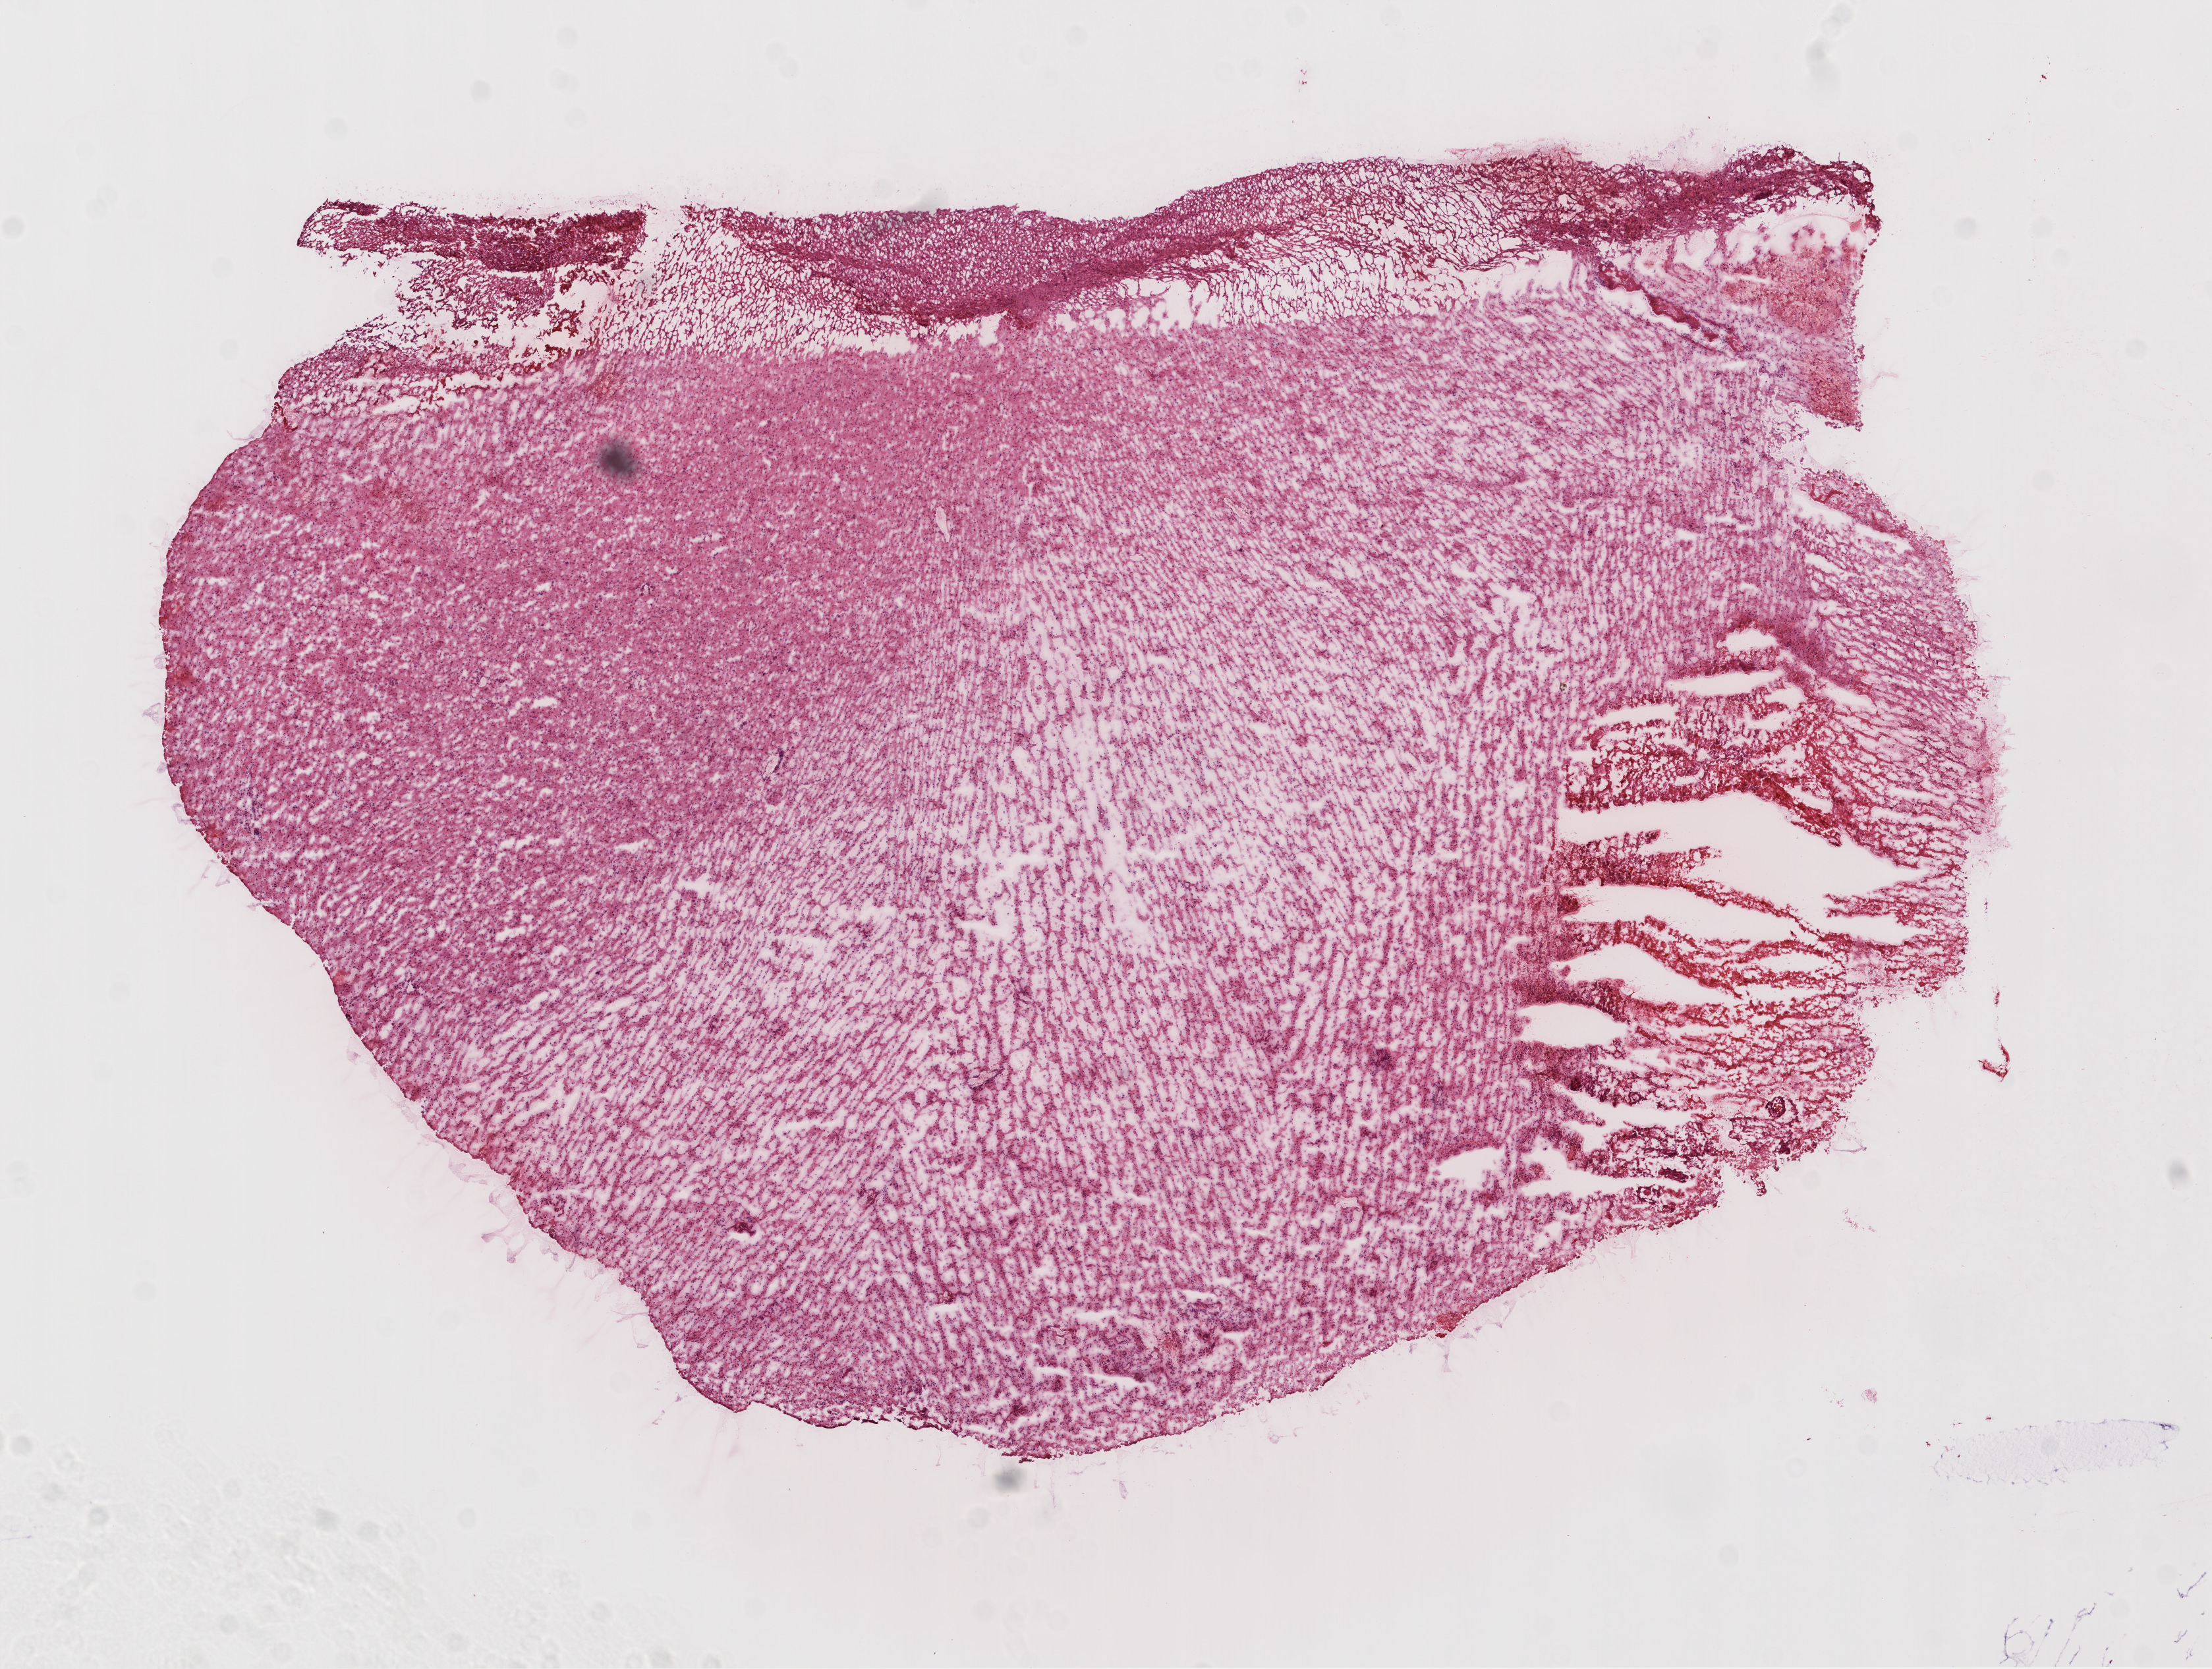
H&E-stained whole-slide image, low-resolution overview of the scanned area, about 13.5 x 10.2 mm (slide scanned at 20x); frozen section; brain, primary tumour sample. Patient: male, age at initial diagnosis 55 years. Pathologist review of this section (percent, as recorded): tumour cells 85%, tumour nuclei 90%, normal cells 5%, stromal cells 10%, necrosis 0%.
• diagnosis: Glioblastoma